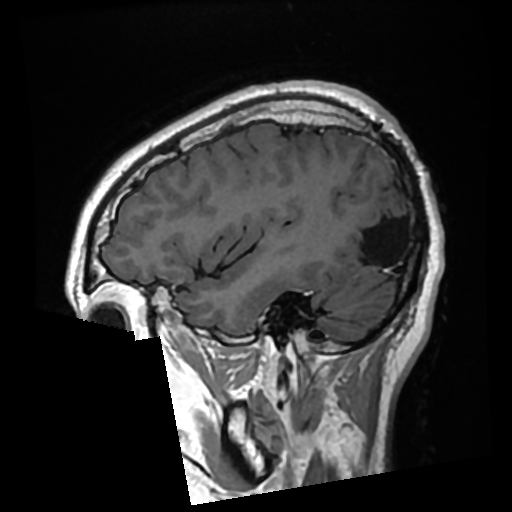
Brain MRI from a brain-tumour surgery series, one sagittal slice; slice 82 of 276 in the series (ordered by position); T1-weighted post-contrast; 0.7 mm slice thickness; 512 × 512 image matrix, field of view 250 × 250 mm. Case-level facts recorded for this patient, not image findings: histopathology: Glioma with ependymal features; WHO grade: 2; tumour location: Left Parietal.
Annotated regions visible in this slice (expert manual segmentation):
- previous resection cavity: bounding box [x1, y1, x2, y2] px = [348, 186, 402, 266]